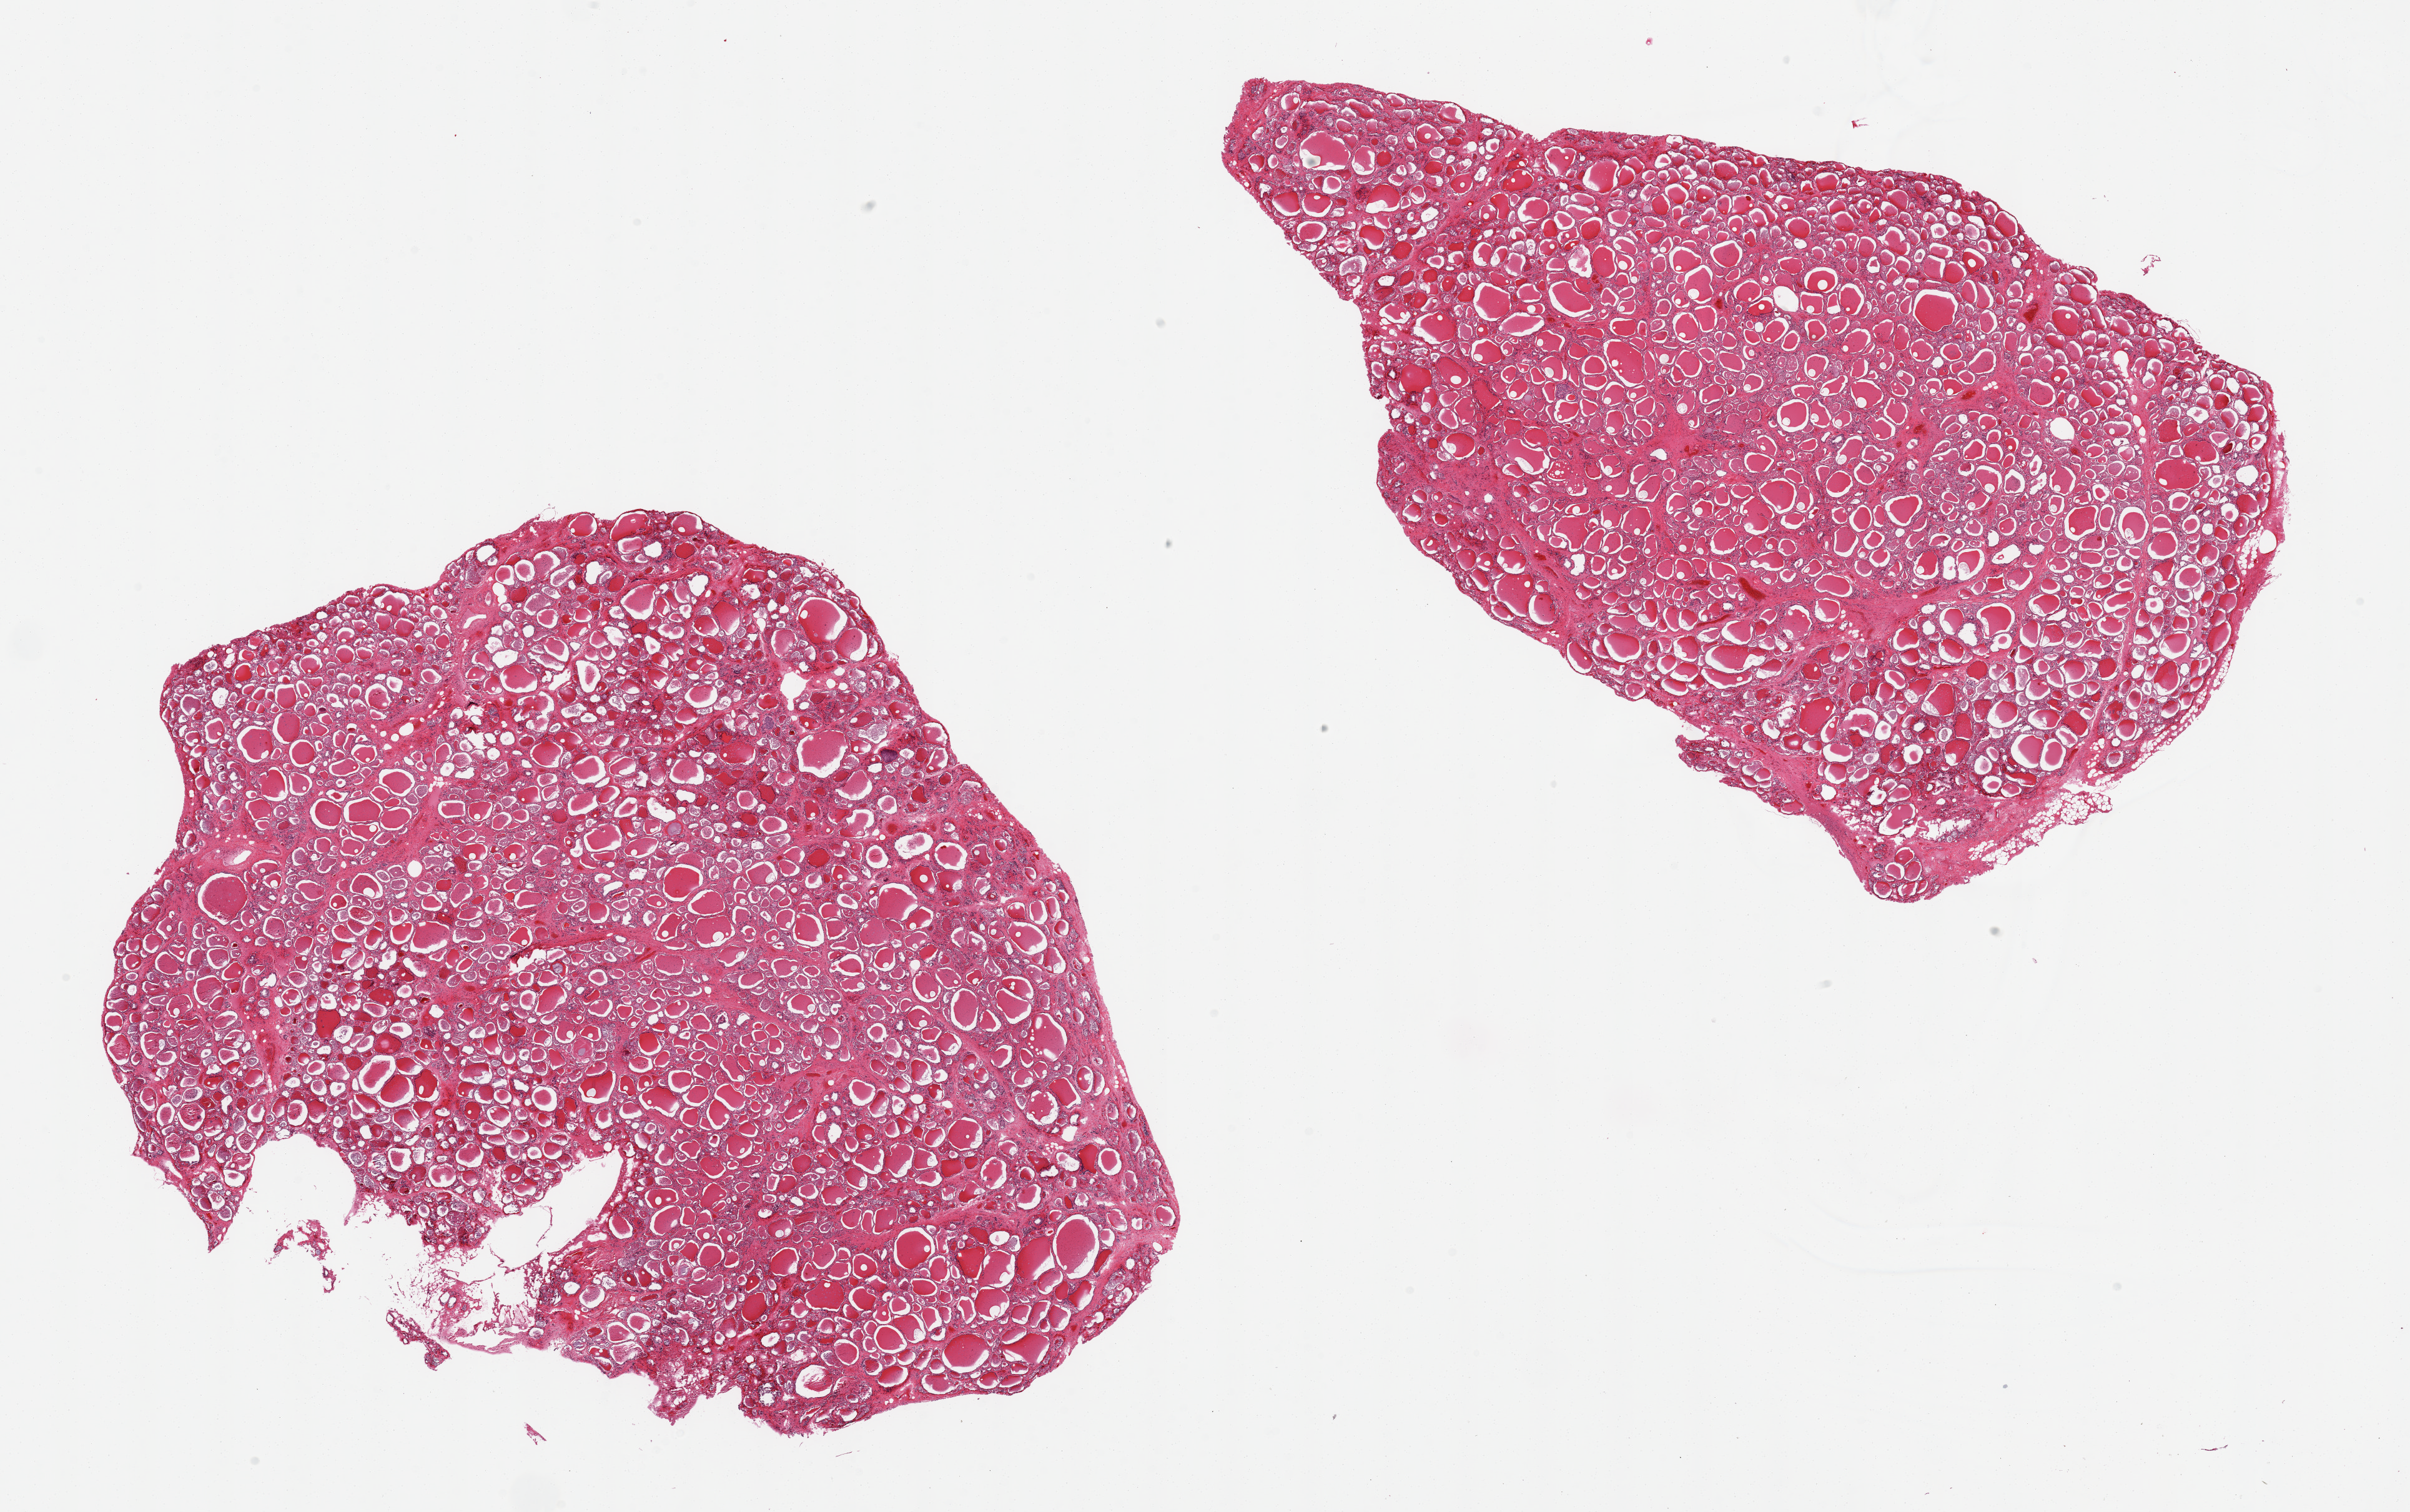
Haematoxylin and eosin whole-slide image, a low-resolution overview of the entire scanned area, about 30.5 x 19.1 mm (acquisition: 20x scan). PAXgene-fixed paraffin-embedded (PFPE) section. Section of thyroid (target tissue). Donor tissue sample.
- reviewer comment on this tissue sample: 2 pieces, no significant abnormalities